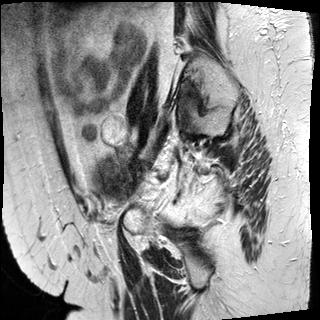
Pelvic MRI for cervical cancer, one sagittal slice; slice 15 of 50 in the series (ordered by position); T2-weighted; 1.5 T; TE 89 ms, TR 4880 ms; 4 mm slice thickness; 320 × 320 image matrix, field of view 260 × 260 mm. Female patient, age 50 years.
Annotated regions visible in this slice (outlined manually by an expert reader):
- uterus and cervix: bounding box [x1, y1, x2, y2] px = [94, 153, 147, 202]